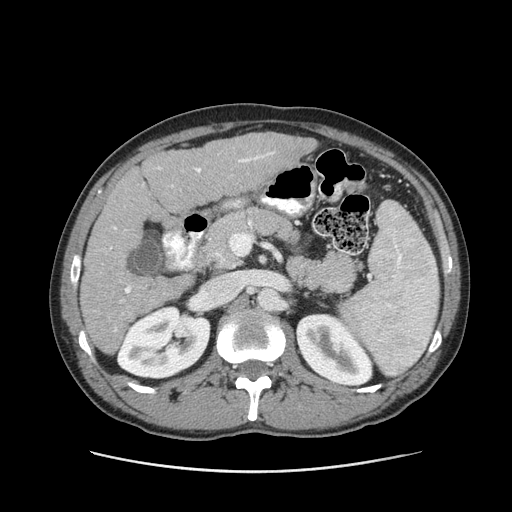
Contrast-enhanced abdominal CT (liver protocol), one axial slice. Reconstruction kernel STANDARD. 120 kVp. Soft-tissue window (W 400 / L 40 HU). 2.5 mm slice thickness. 512 × 512 image matrix. From the clinical record (not read from this slice): diagnosis: hepatocellular carcinoma (patient treated with transarterial chemoembolisation; whether this scan precedes or follows treatment is not stated here); TNM stage (as recorded): Stage-II; Child-Pugh class: A.
Outlined on this slice (semi-automatic segmentation, software-assisted and operator-edited):
- liver parenchyma outside the tumour (the mass and vessels are separate outlines, so this box may not span the whole liver): box from (x=80, y=132) to (x=317, y=354) px
- liver vessels: (x=110, y=152)–(x=274, y=331)